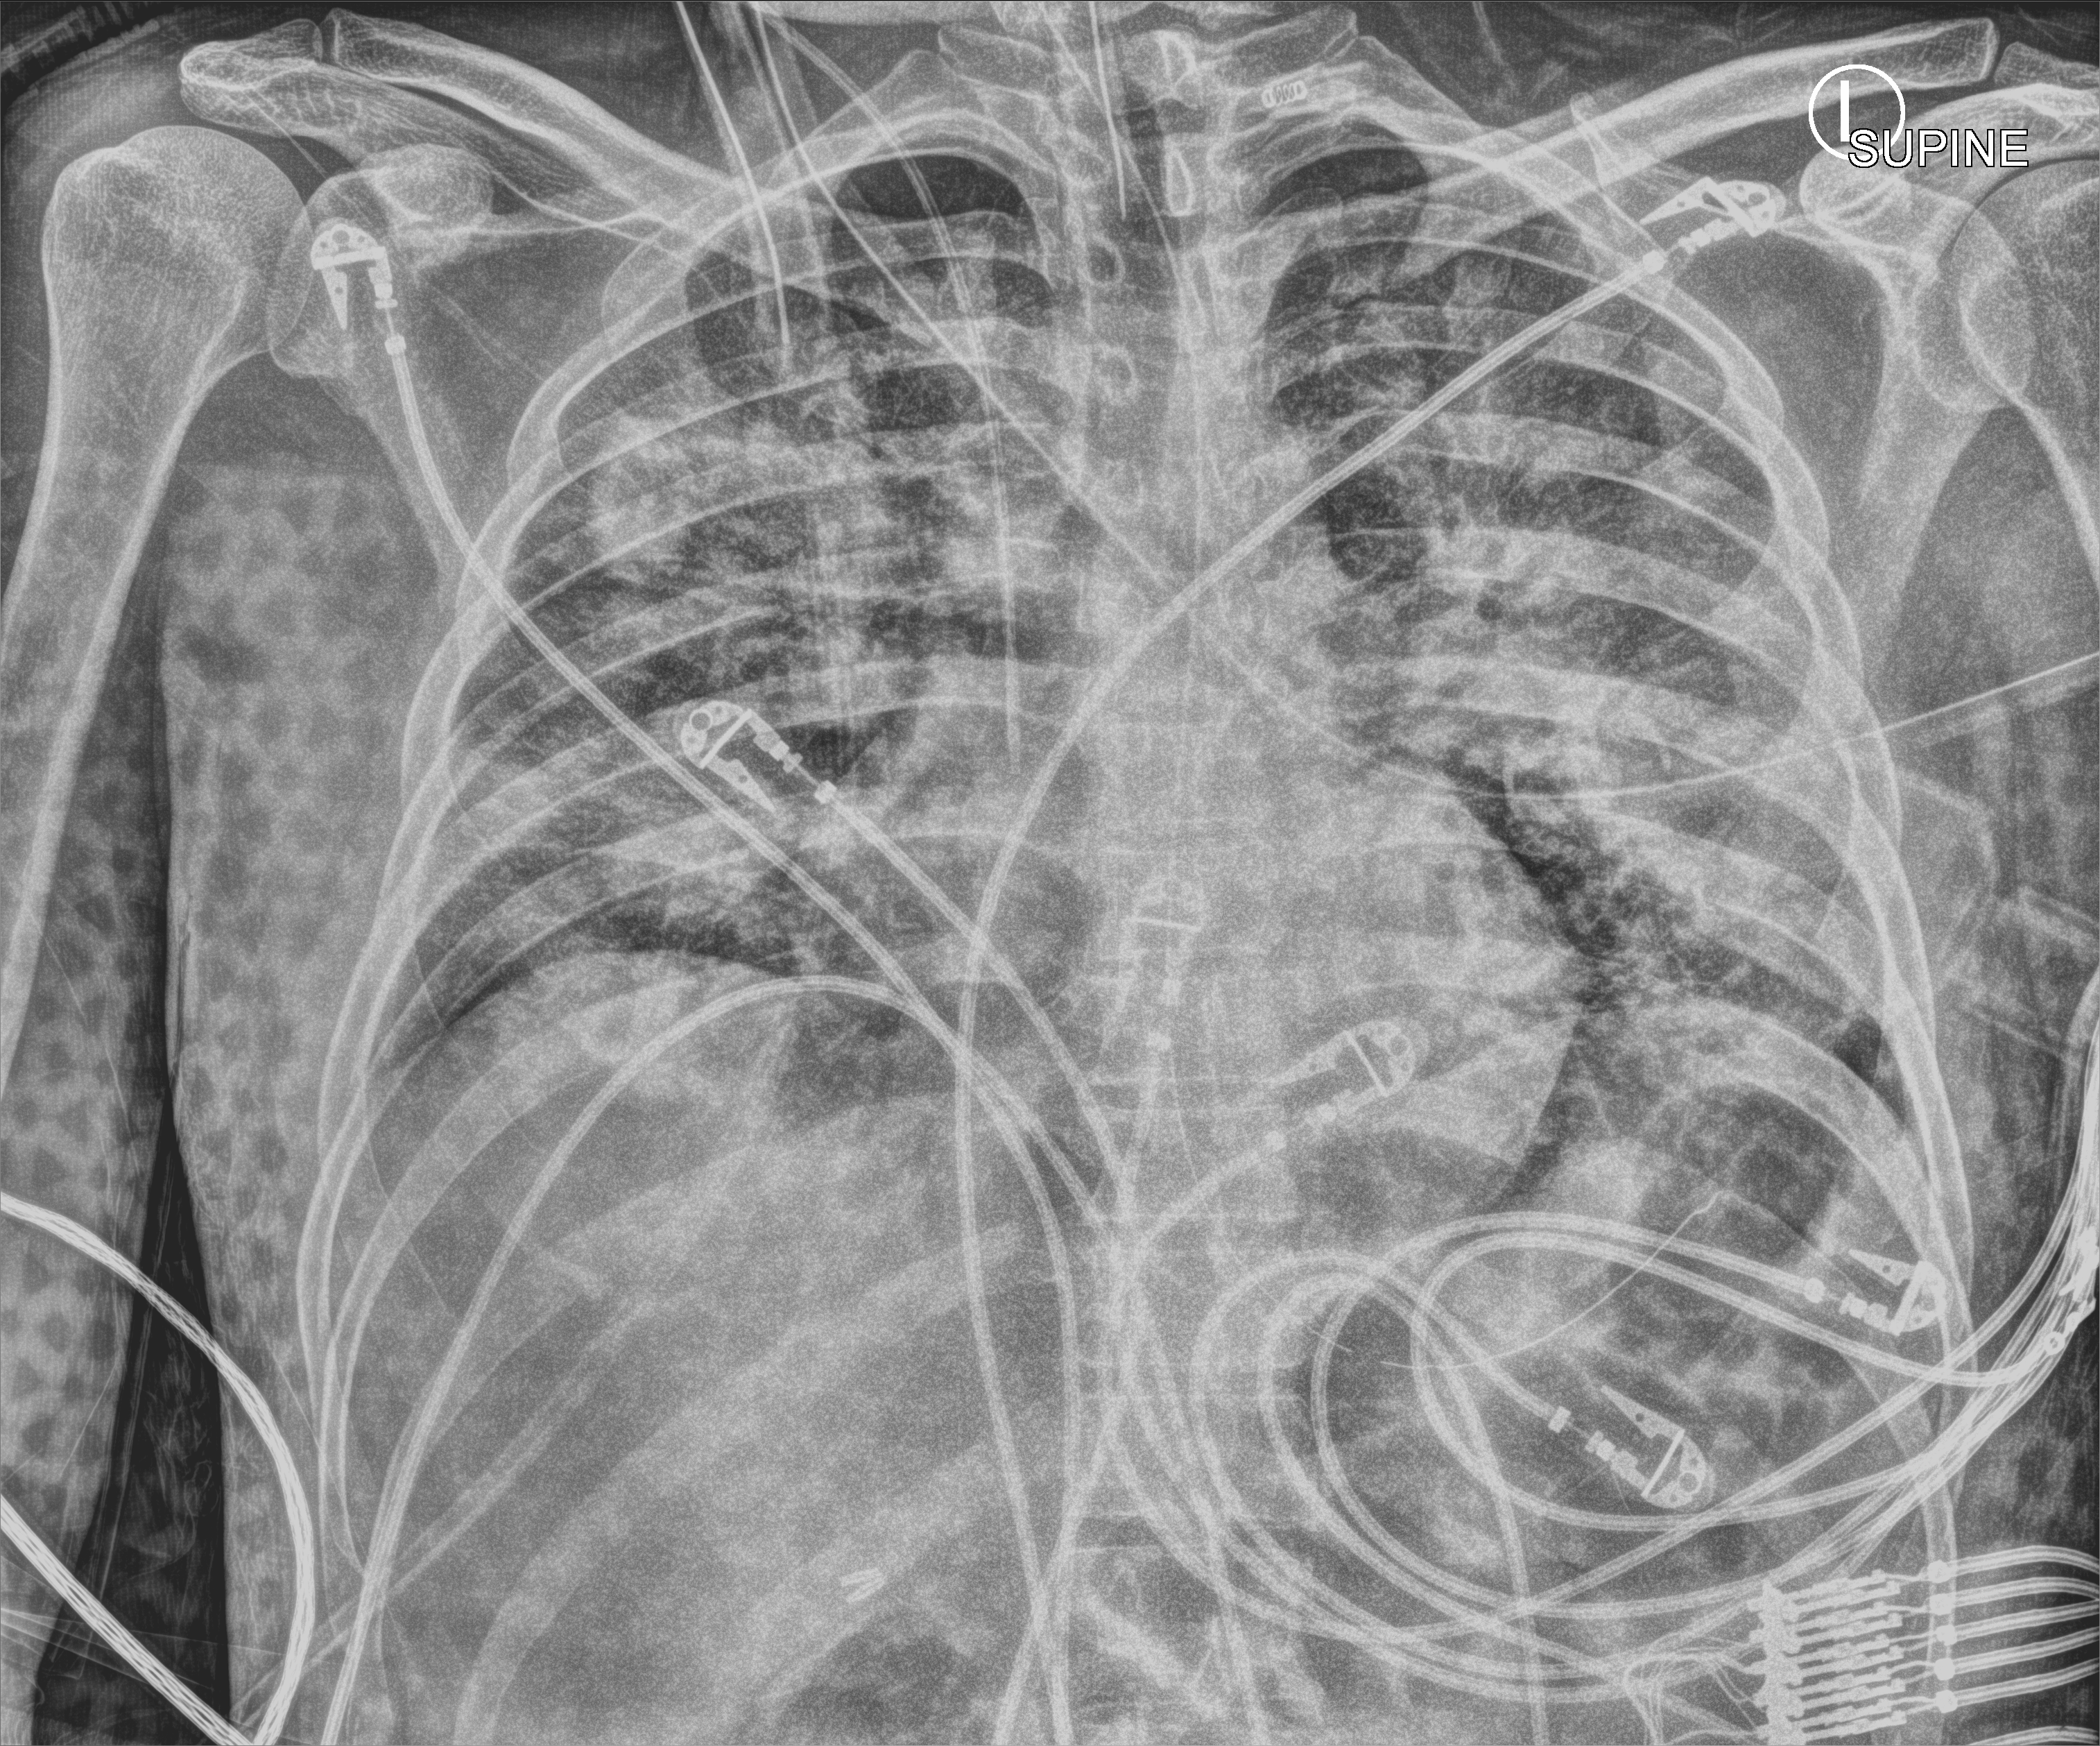
Chest X-ray (portable), anteroposterior (AP) projection. Male patient hospitalised with COVID-19, age 18–59 years.
From the hospital-stay record, not from the radiograph (when in the stay this image was taken is not recorded): length of hospital stay: 29 days.